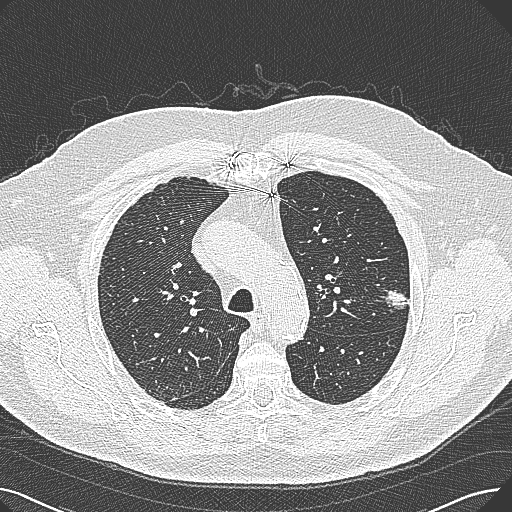
Low-dose screening chest CT, axial slice; baseline screening round; lung window (W 1500 / L -600 HU); 1 mm slice thickness; lung (sharp) reconstruction kernel (B80f); 512 × 512 image matrix. Male participant, aged 74 years at enrolment.
Lesion marked by an expert reader, bounding box [x1, y1, x2, y2] px = [374, 273, 424, 318]. Reader record for this screening exam (exam-level; its link to the box is not recorded): non-calcified nodule or mass ≥4 mm, left upper lobe, 15 × 10 mm, poorly defined margins, soft tissue attenuation. Official screen result: positive, change unspecified: nodule(s) >= 4 mm or enlarging nodule(s), mass(es), or other non-specific abnormalities suspicious for lung cancer. Participant outcome: lung cancer diagnosed 124 days after this screen — adenocarcinoma, NOS, left upper lobe, well differentiated (G1), stage IA (AJCC 6th edition), 26 mm at pathology.